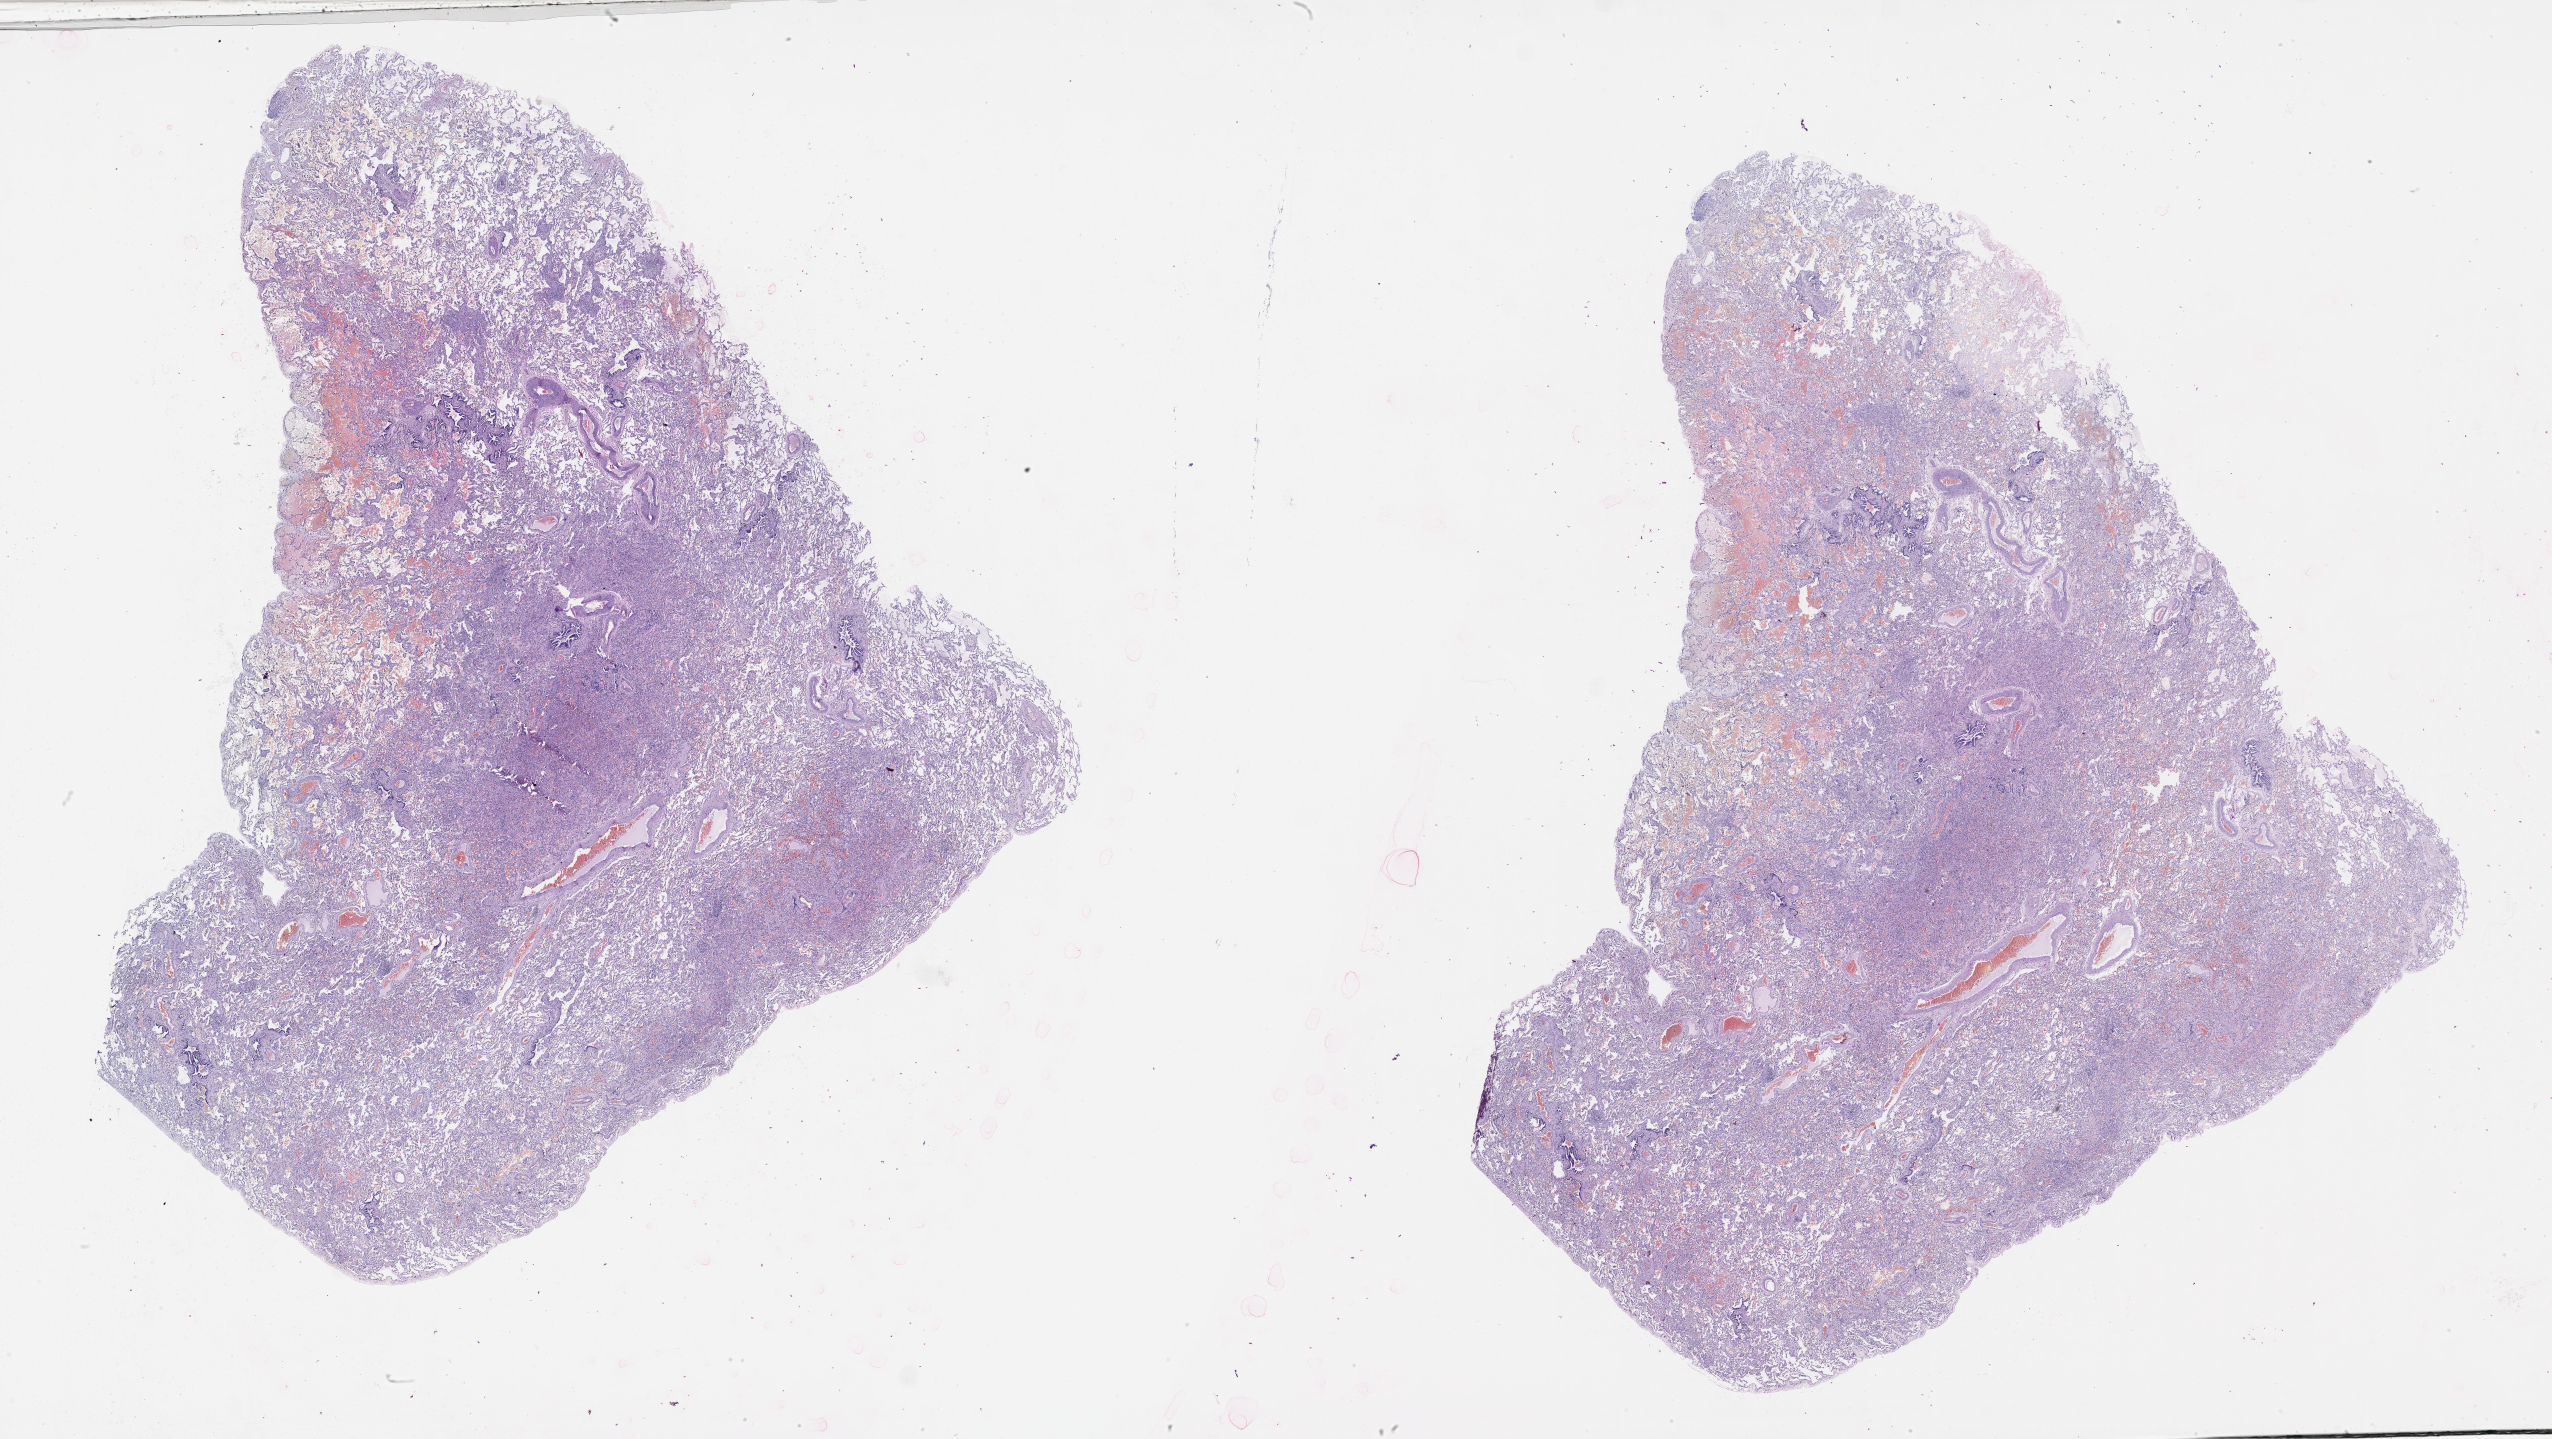
Digitized H&E tissue section (whole slide), a low-resolution overview of the entire scanned area, about 41.1 x 23.2 mm. Lung, normal (non-tumour) tissue. Female, 62 y/o.
- this section: normal (non-tumour) tissue from the same patient
- patient diagnosis (cohort enrolment): squamous cell carcinoma (lung)